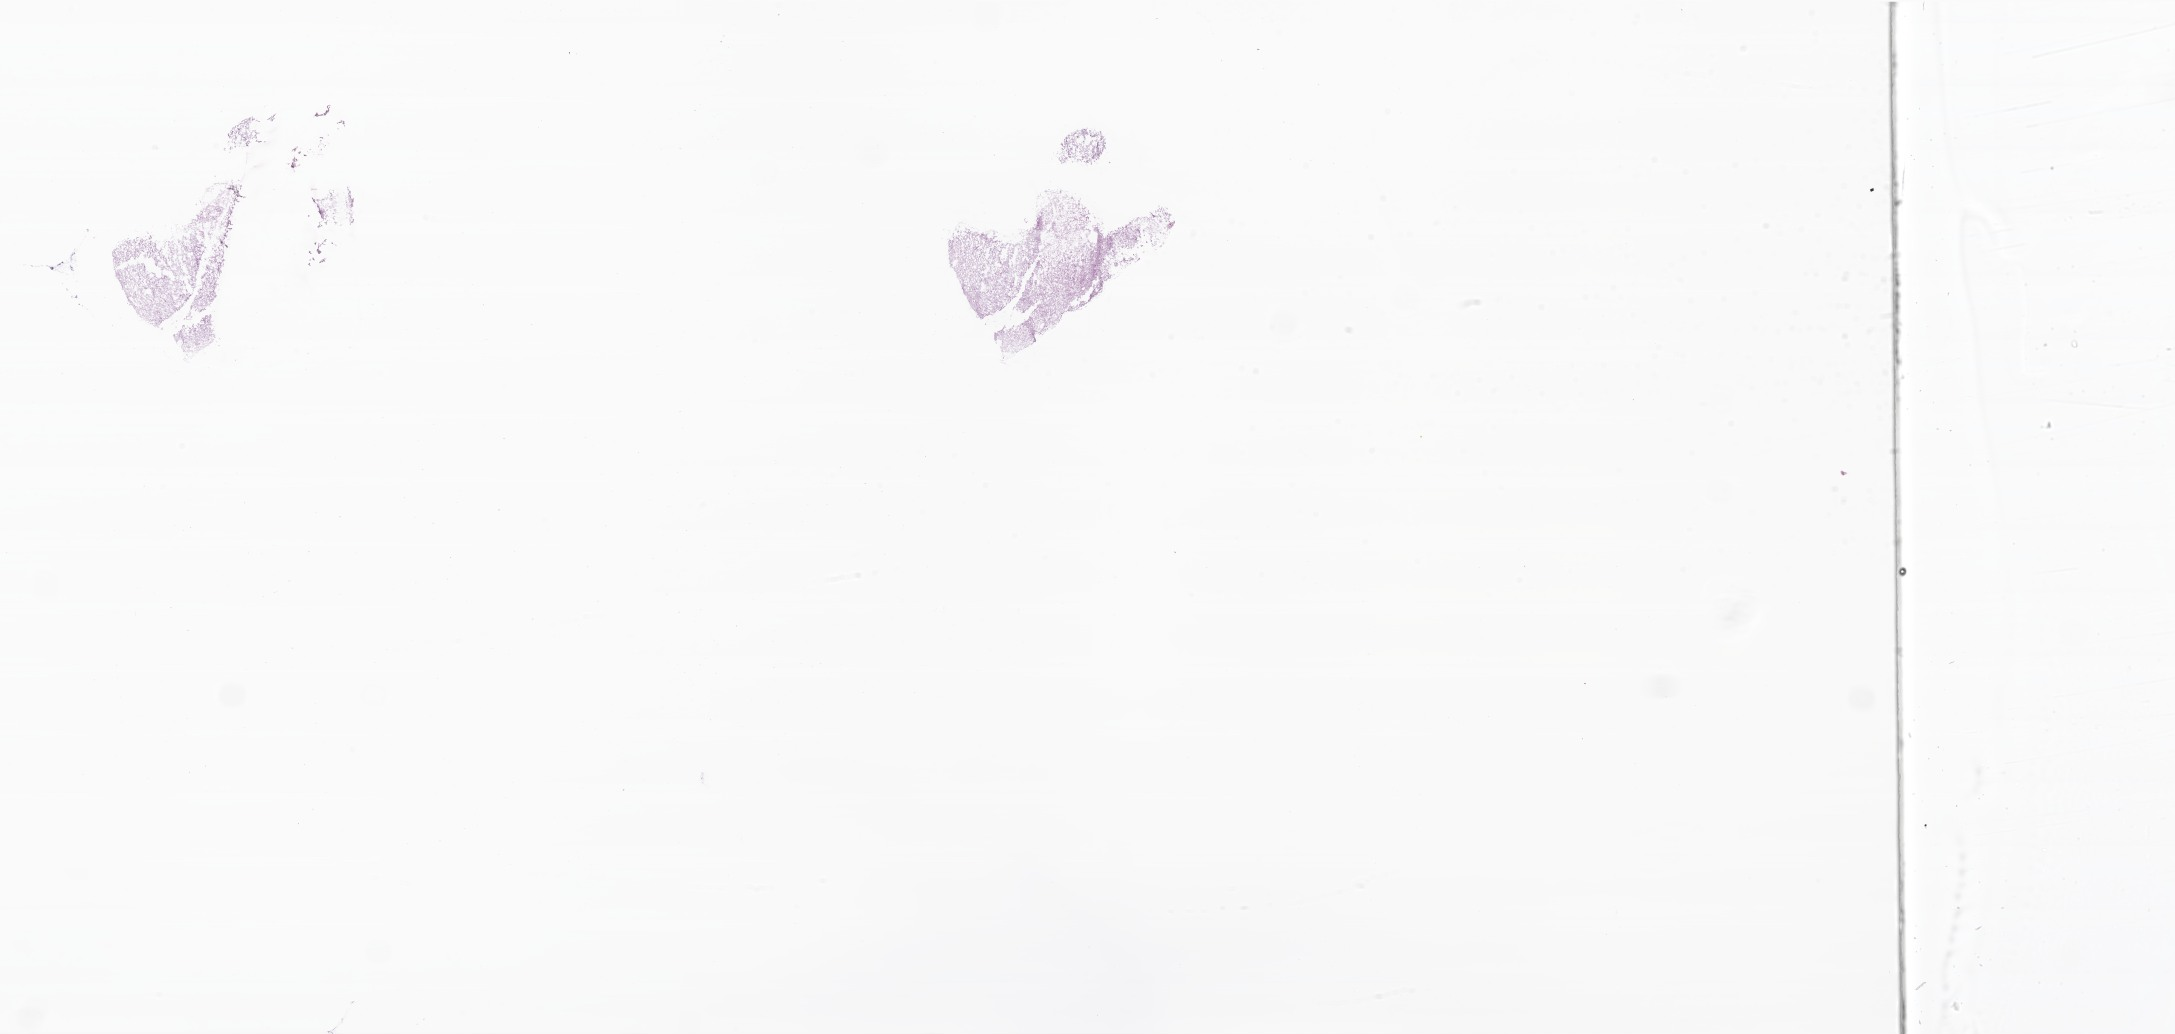
Whole-slide image, haematoxylin and eosin stain of tumor tissue from the brain, a low-resolution overview of the entire scanned area, about 36.7 x 17.4 mm, frozen section (OCT-embedded). Female patient, age 123 months (10 years 3 months).
• recorded diagnosis: Glioma, malignant